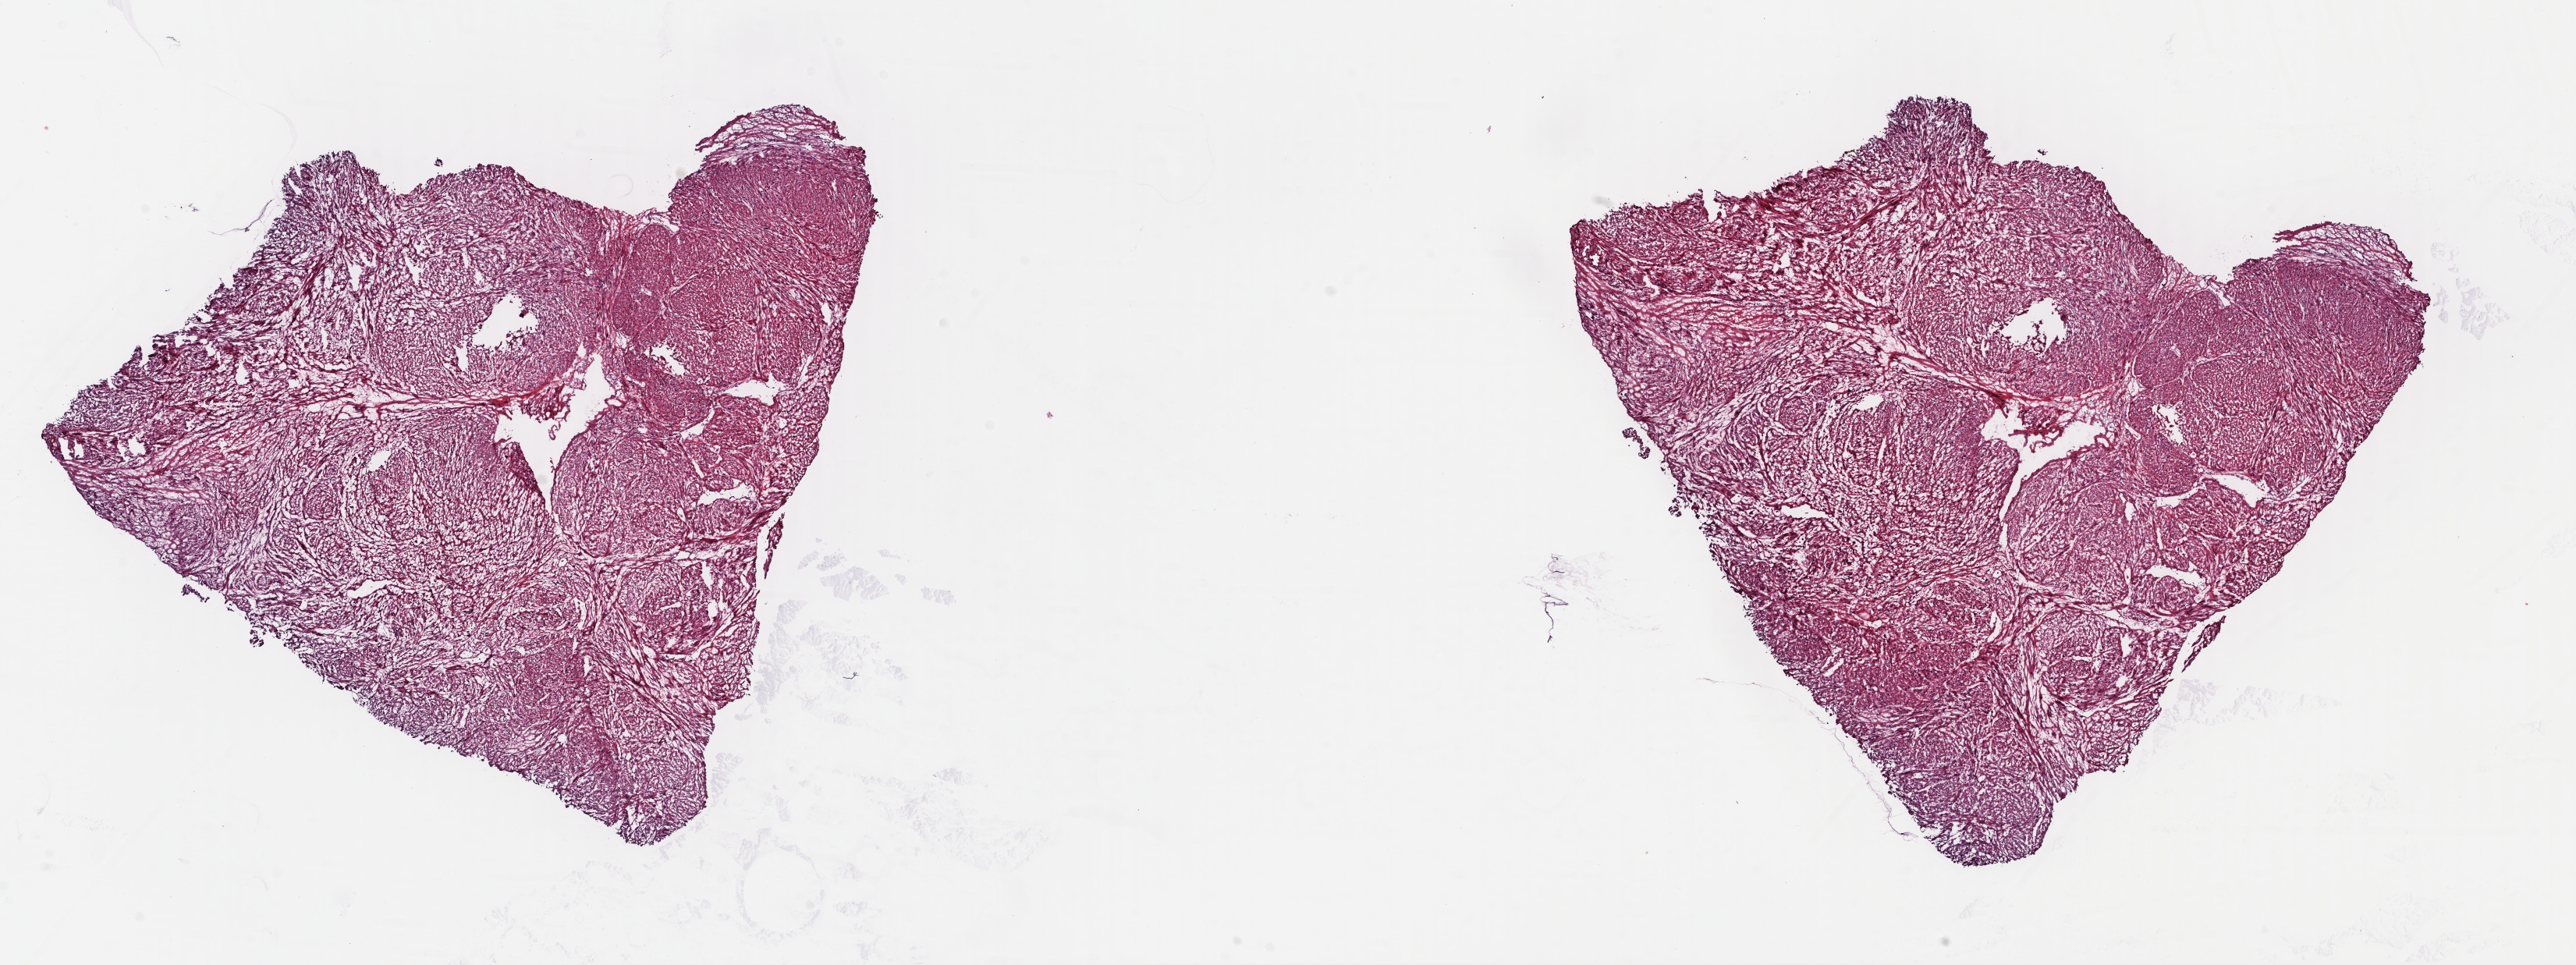
Digitized H&E-stained tissue section (whole slide), low-resolution overview of the scanned area, about 26.0 x 9.7 mm (acquisition: 40x scan). Frozen section from the top of the tissue portion. Primary tumour sample from the retroperitoneum and peritoneum. Female patient; age at initial diagnosis 72 years. Pathologist review of this section (percent, as recorded): tumour cells 85%, tumour nuclei 100%, normal cells 0%, stromal cells 15%, necrosis 0%. Infiltration values recorded for this section: lymphocyte infiltration 0%, monocyte infiltration 0%, neutrophil infiltration 0%.
Histologic diagnosis: Leiomyosarcoma, NOS (retroperitoneum).